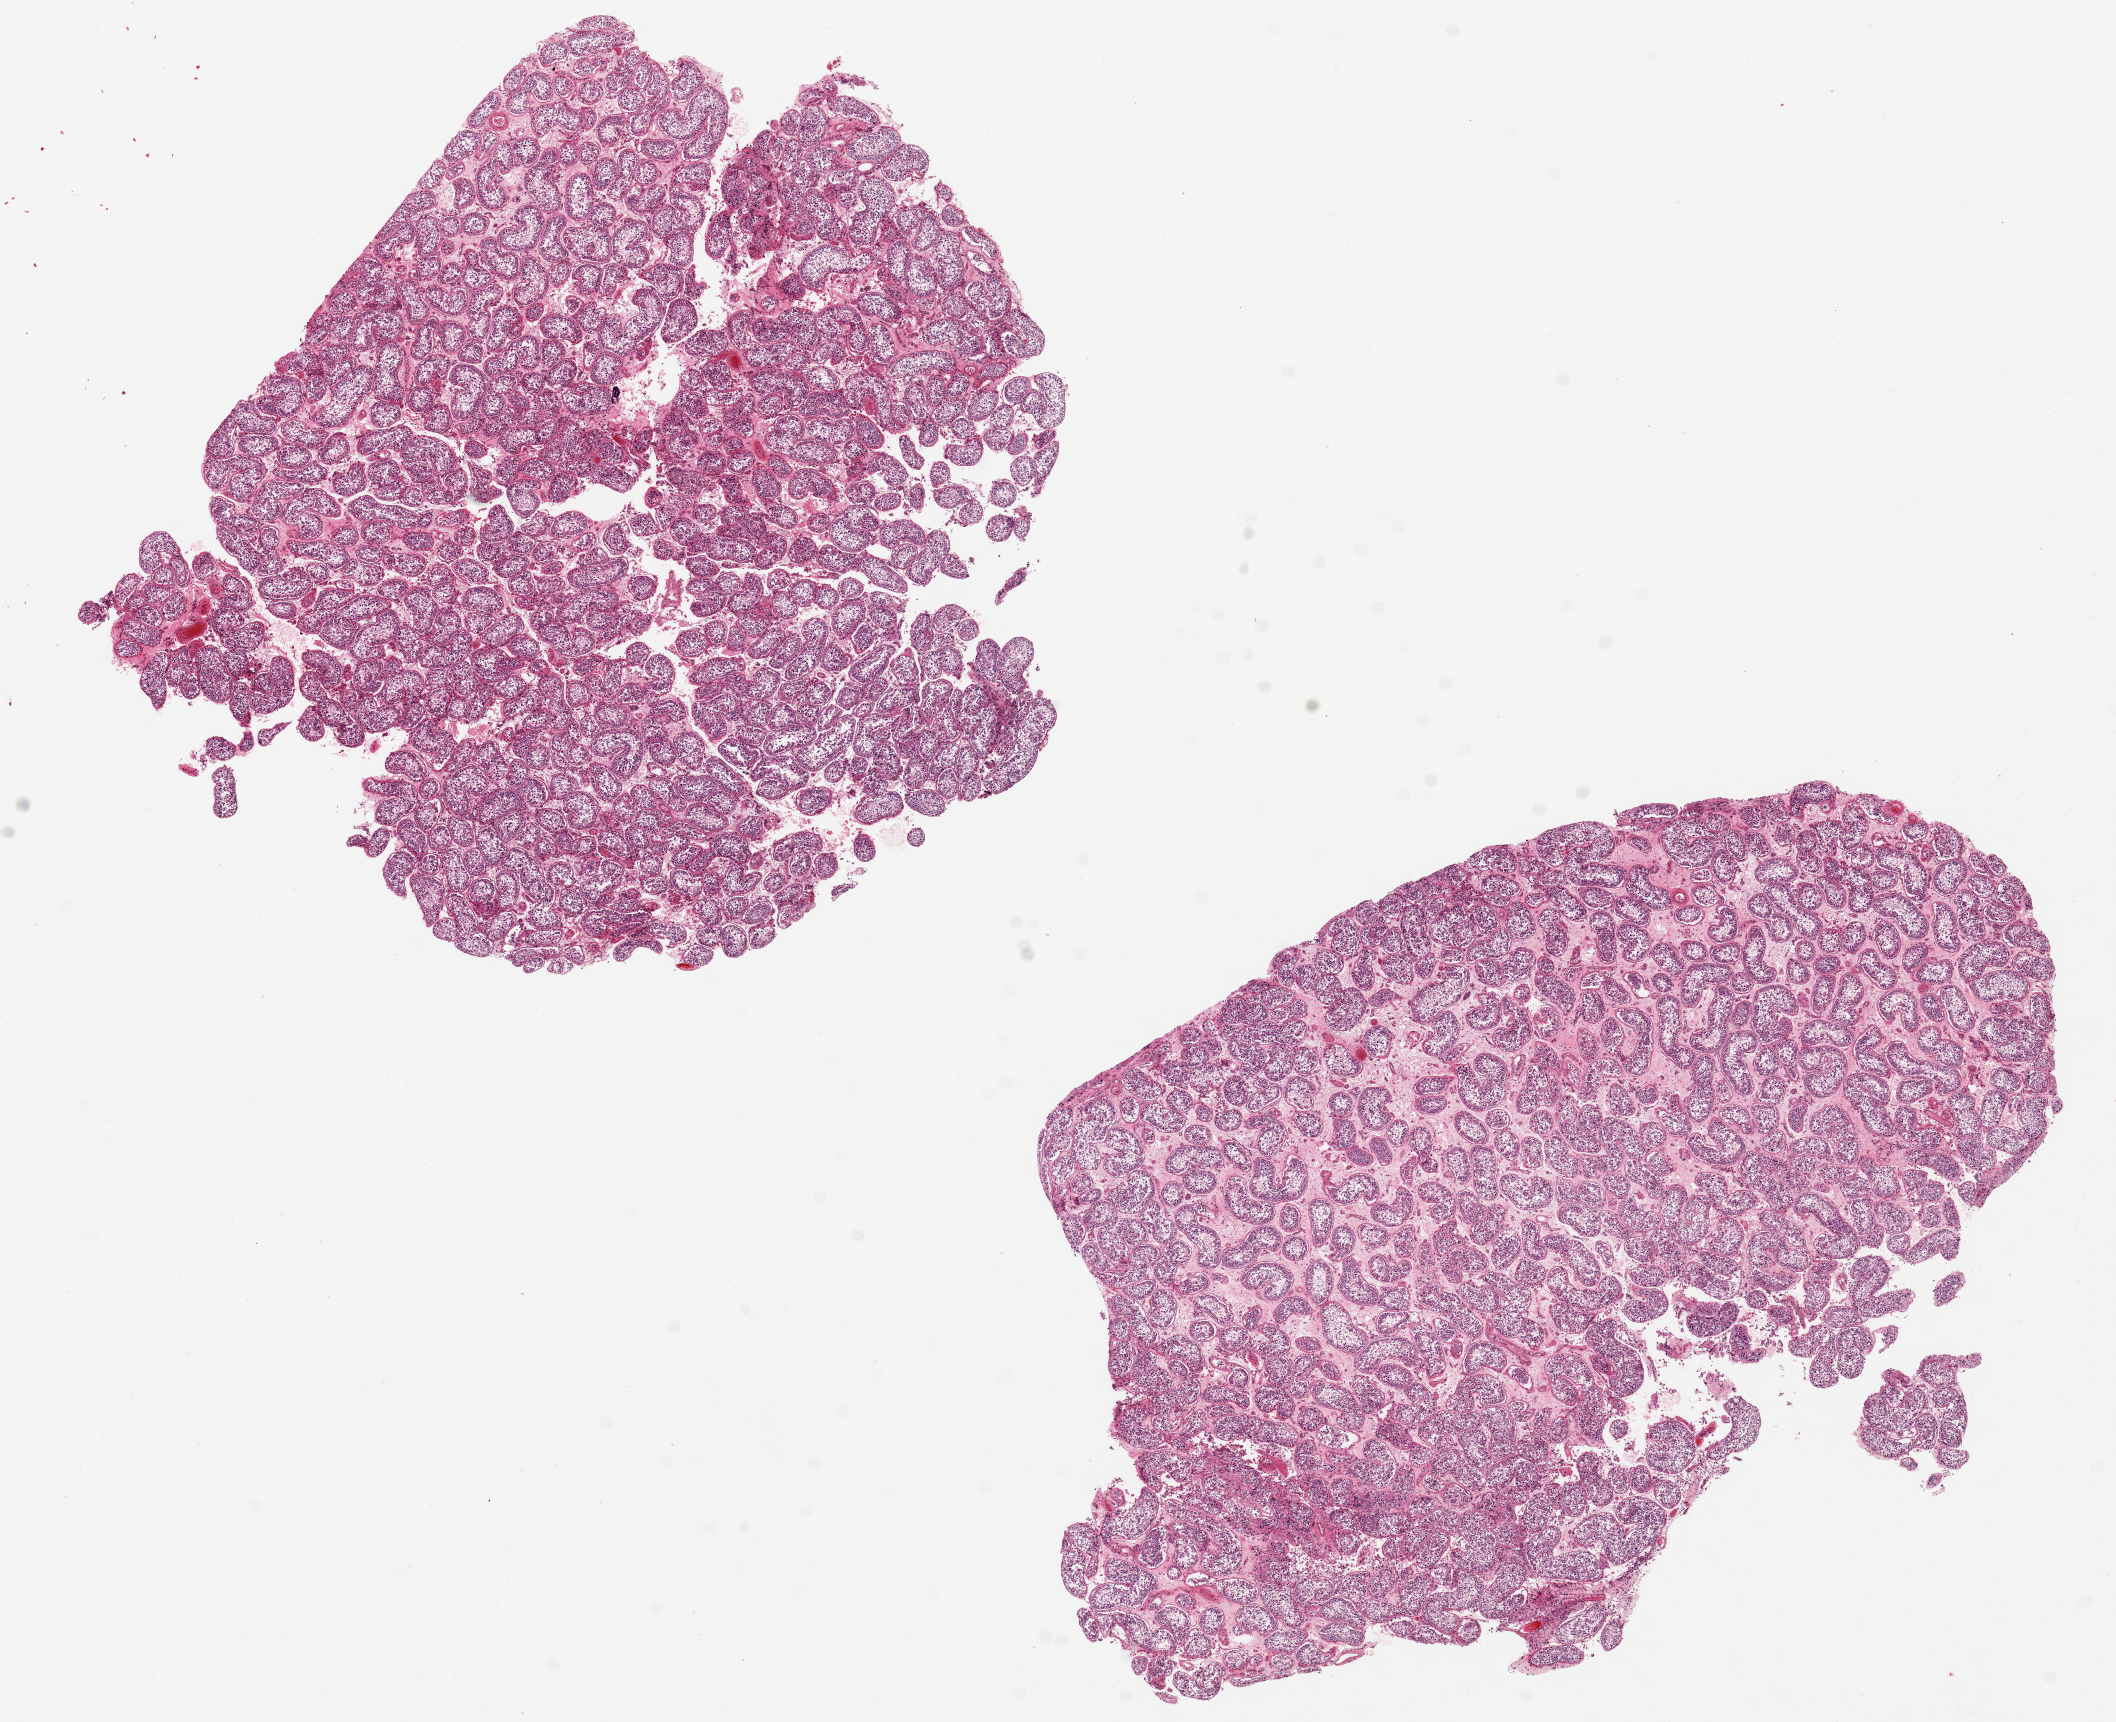
H&E whole-slide image, whole scanned area (about 16.7 x 13.6 mm) shown as a low-resolution overview. PAXgene-fixed paraffin-embedded (PFPE) section. Target tissue: testis. Tissue donor sample. Donor sex: male.
Pathologist's review note for this sample: 2 pieces ~,permatogenesis is present.